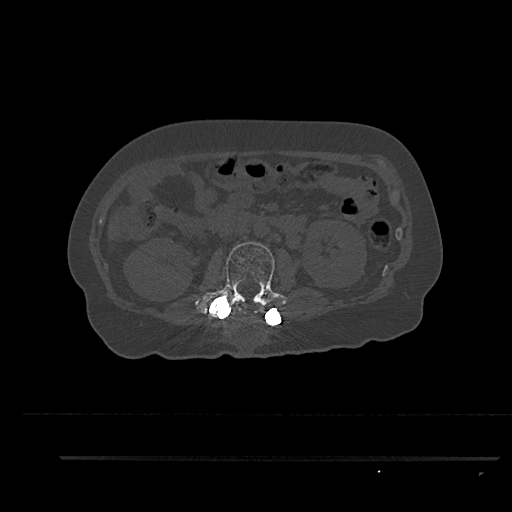
CT including the spine, one axial slice; slice 158 of 797 in the series (ordered by position); 120 kVp; bone window (W 1800 / L 400 HU); 0.5 mm slice thickness; 512 × 512 image matrix, field of view 408 × 408 mm. Patient: female, 44 years. Case-level facts recorded for this patient, not image findings: primary cancer: renal.
Outlined on this slice (semi-automatically segmented with operator editing):
- L2 vertebra: box from (x=195, y=241) to (x=285, y=320) px